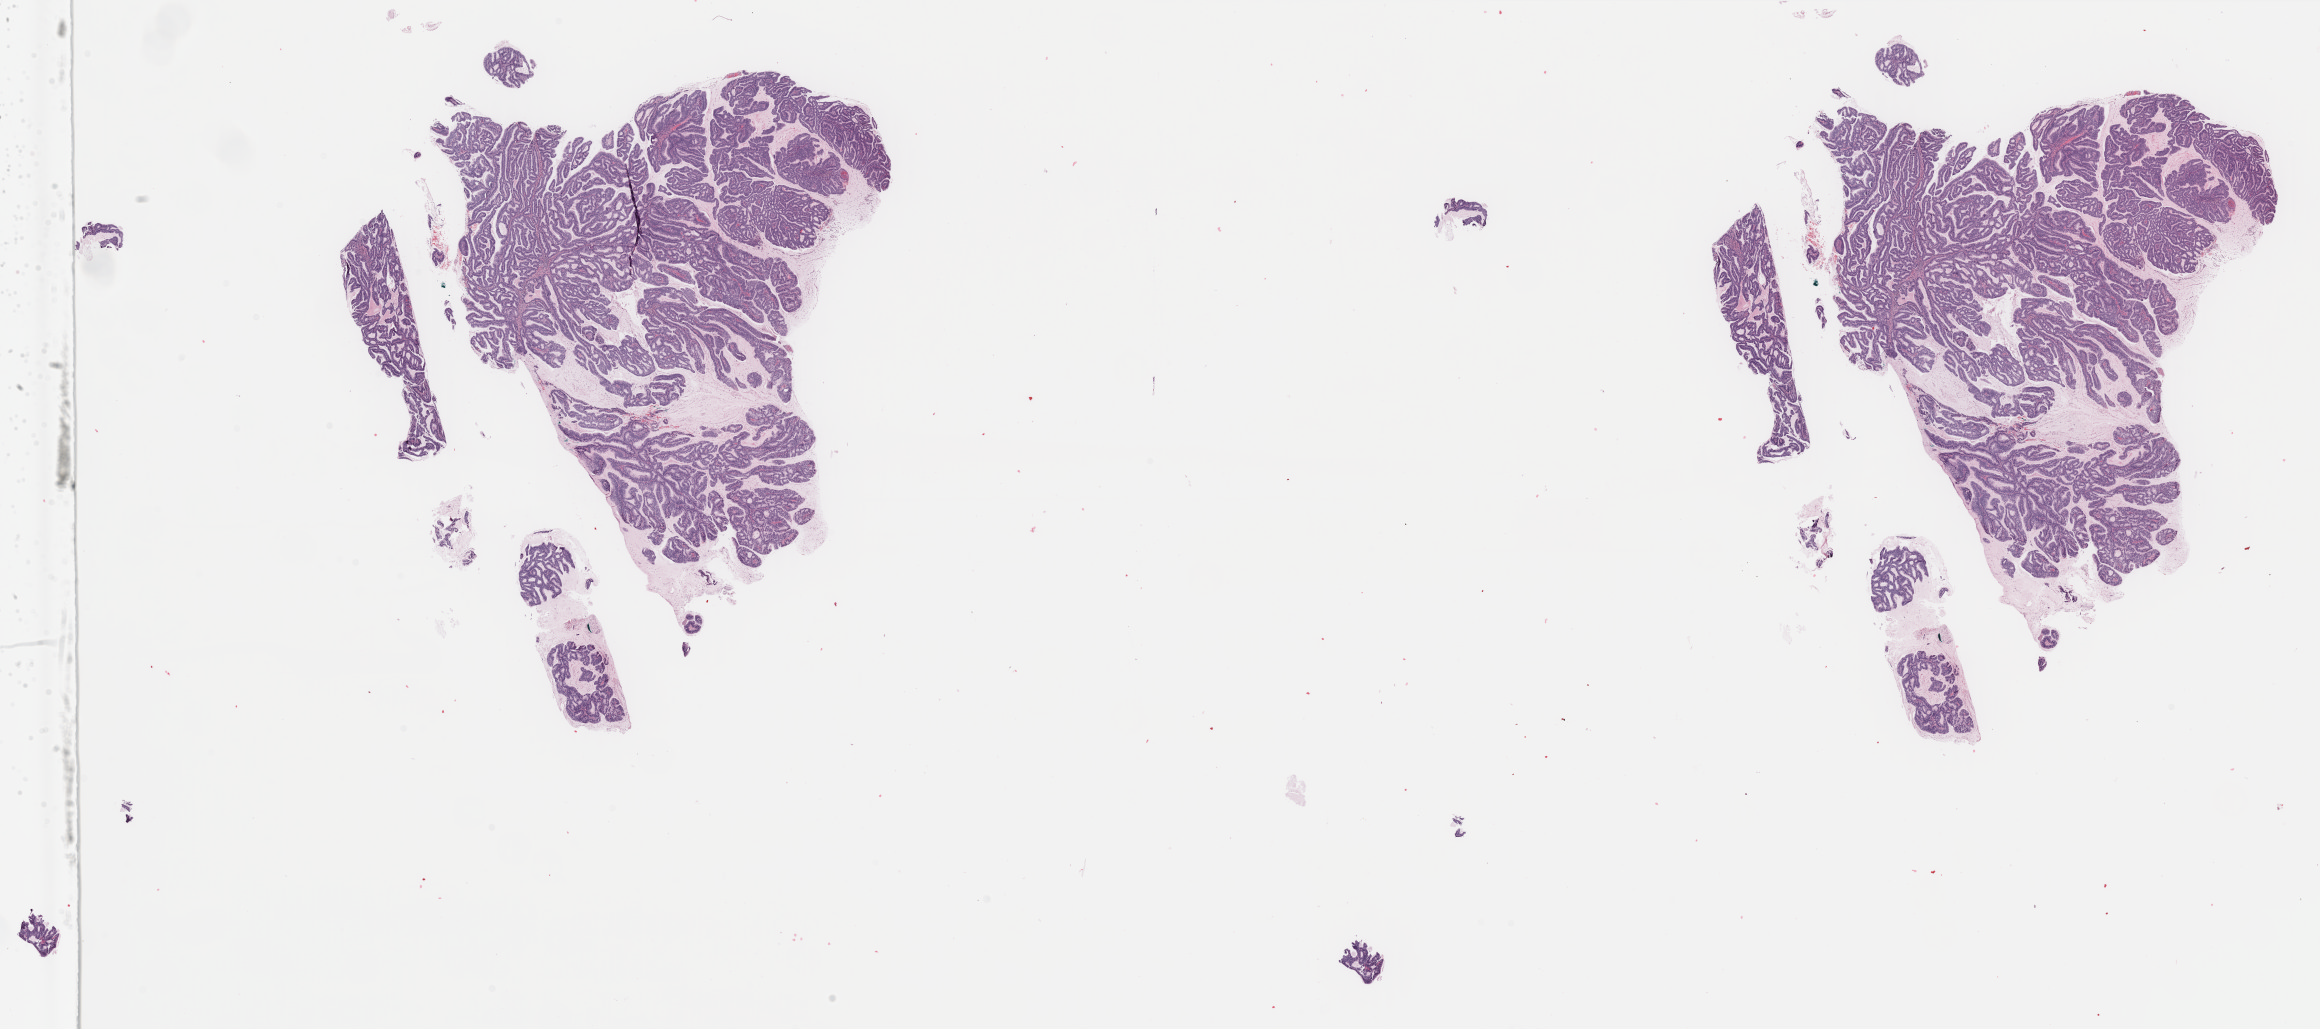
Whole-slide histology image, H&E, whole scanned area (about 36.7 x 16.3 mm) shown as a low-resolution overview, FFPE section, cervix, primary tumour sample. Female, age 42 years at initial diagnosis. Histologic grade: G1 (well differentiated).
TNM: T1b1 NX M1. AJCC pathologic stage: IVB. Diagnosis: Adenocarcinoma, endocervical type (cervix uteri).